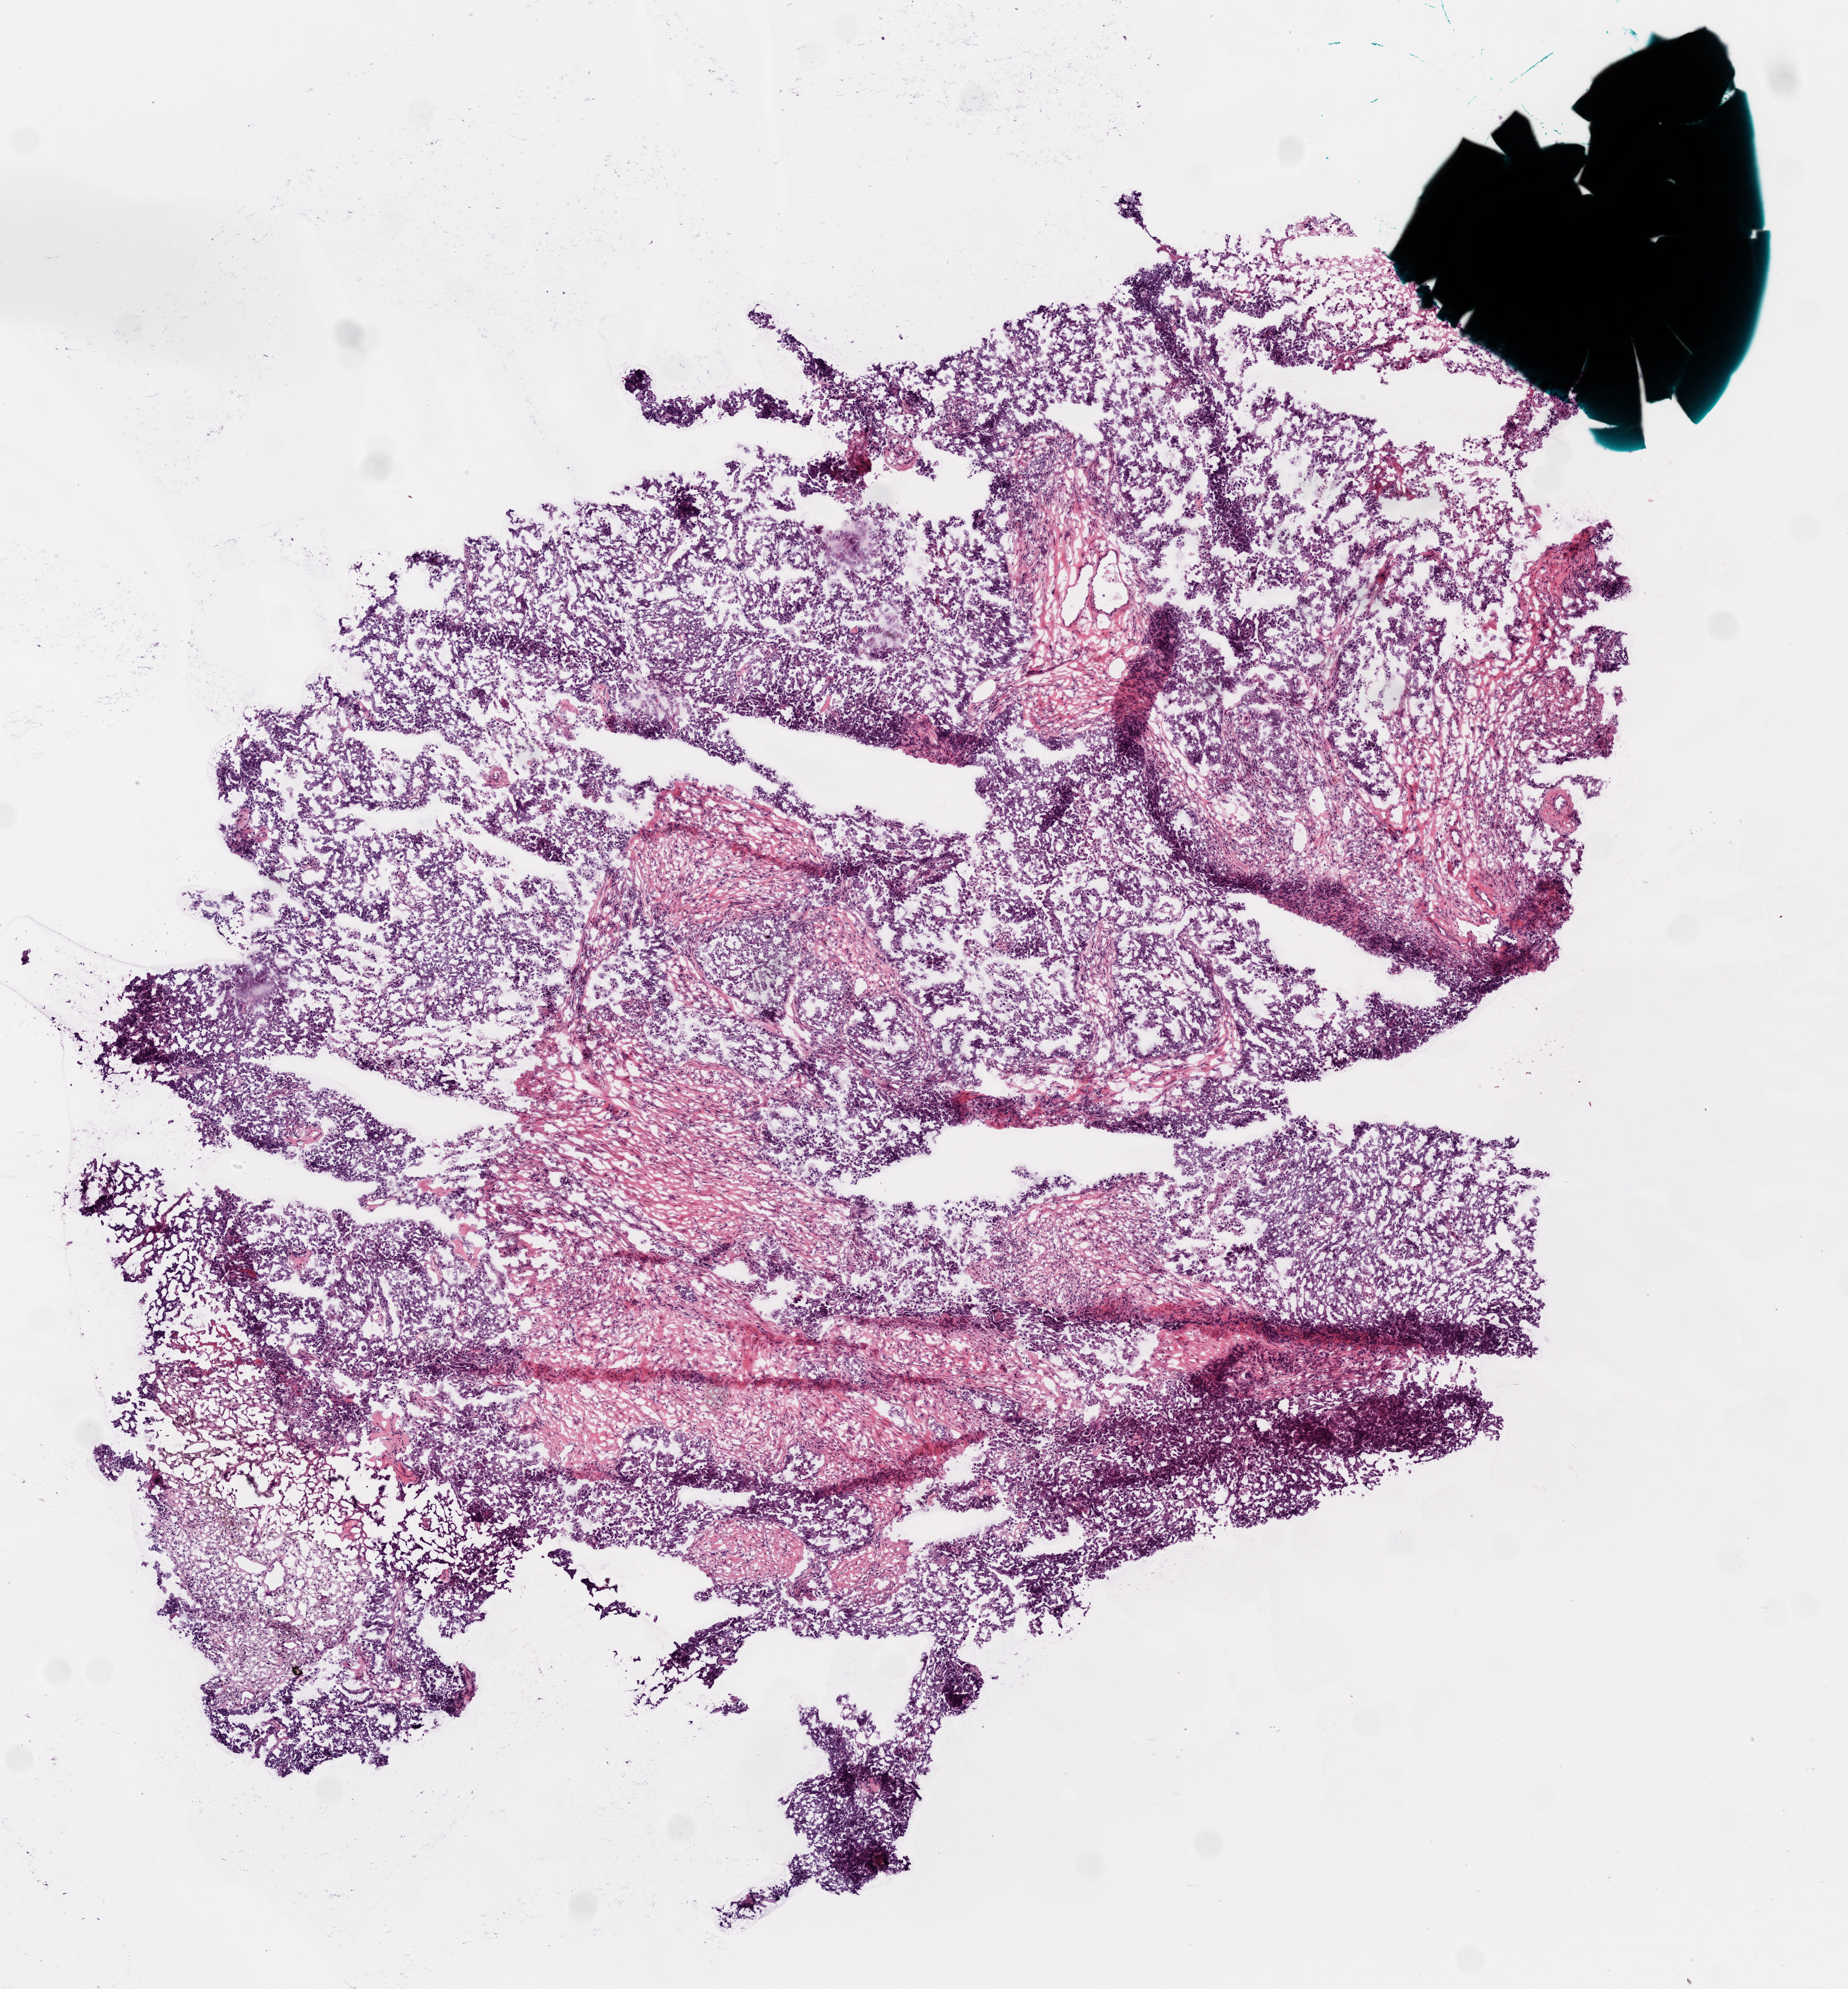
Whole-slide histology image, Hematoxylin and eosin (H&E) stained — a low-resolution overview of the entire scanned area, about 6.3 x 6.8 mm; frozen section from the bottom of the tissue portion; sample: primary tumour, ovary. Patient: female, age at initial diagnosis 59 years. Histologic grade: G3 (poorly differentiated). Pathologist review of this section (percent, as recorded): tumour cells 0%, tumour nuclei 90%, normal cells 0%, stromal cells 0%, necrosis 5%.
* histologic diagnosis: Serous cystadenocarcinoma, NOS
* laterality: left
* FIGO stage: IV